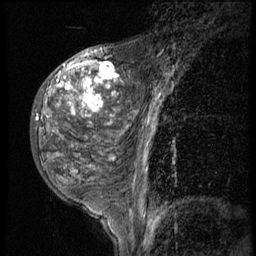
Breast MRI (dynamic contrast-enhanced), one sagittal slice; position 18 of 56 along the scan axis; 3 images stored at this slice position (order not interpretable as contrast timing); 1.5 T; TE 4.2 ms, TR 9 ms; 2.5 mm slice thickness; 256 × 256 image matrix. Patient: female, 50 years. Case-level facts recorded for this patient, not image findings: setting: breast cancer imaged before/during neoadjuvant chemotherapy; receptor status: triple-negative.
Outlined on this slice (semi-automatic segmentation, software-assisted and operator-edited):
- analysis volume of interest (the breast-tissue region the enhancement analysis was run in; not a lesion): box from (x=30, y=50) to (x=117, y=191) px
- tumour enhancement mask (voxels above the 140 % enhancement threshold inside the analysis volume of interest): (x=57, y=62)–(x=116, y=160)